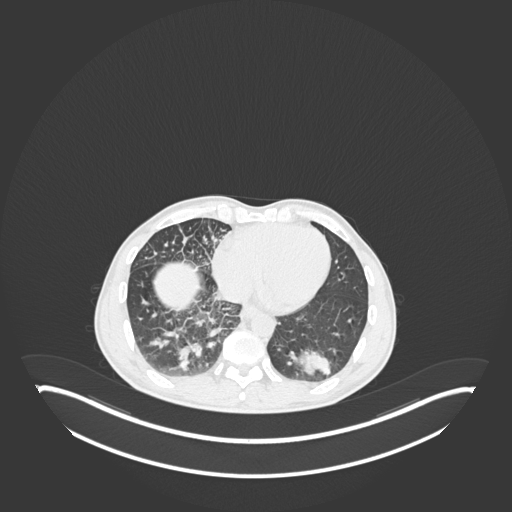
Chest CT, one axial slice; reconstruction kernel B30f; 120 kVp; lung window (W 1500 / L -600 HU); 1 mm slice thickness; 512 × 512 image matrix, field of view 500 × 500 mm. Patient: male, 49 years. From the clinical record (not read from this slice): clinical TNM (as recorded): T2b N1 M0.
Outlined on this slice (rectangle marked by the reading radiologist):
- lung tumour (recorded histology: adenocarcinoma): bounding box <289,345,335,379> (left, top, right, bottom; pixels)